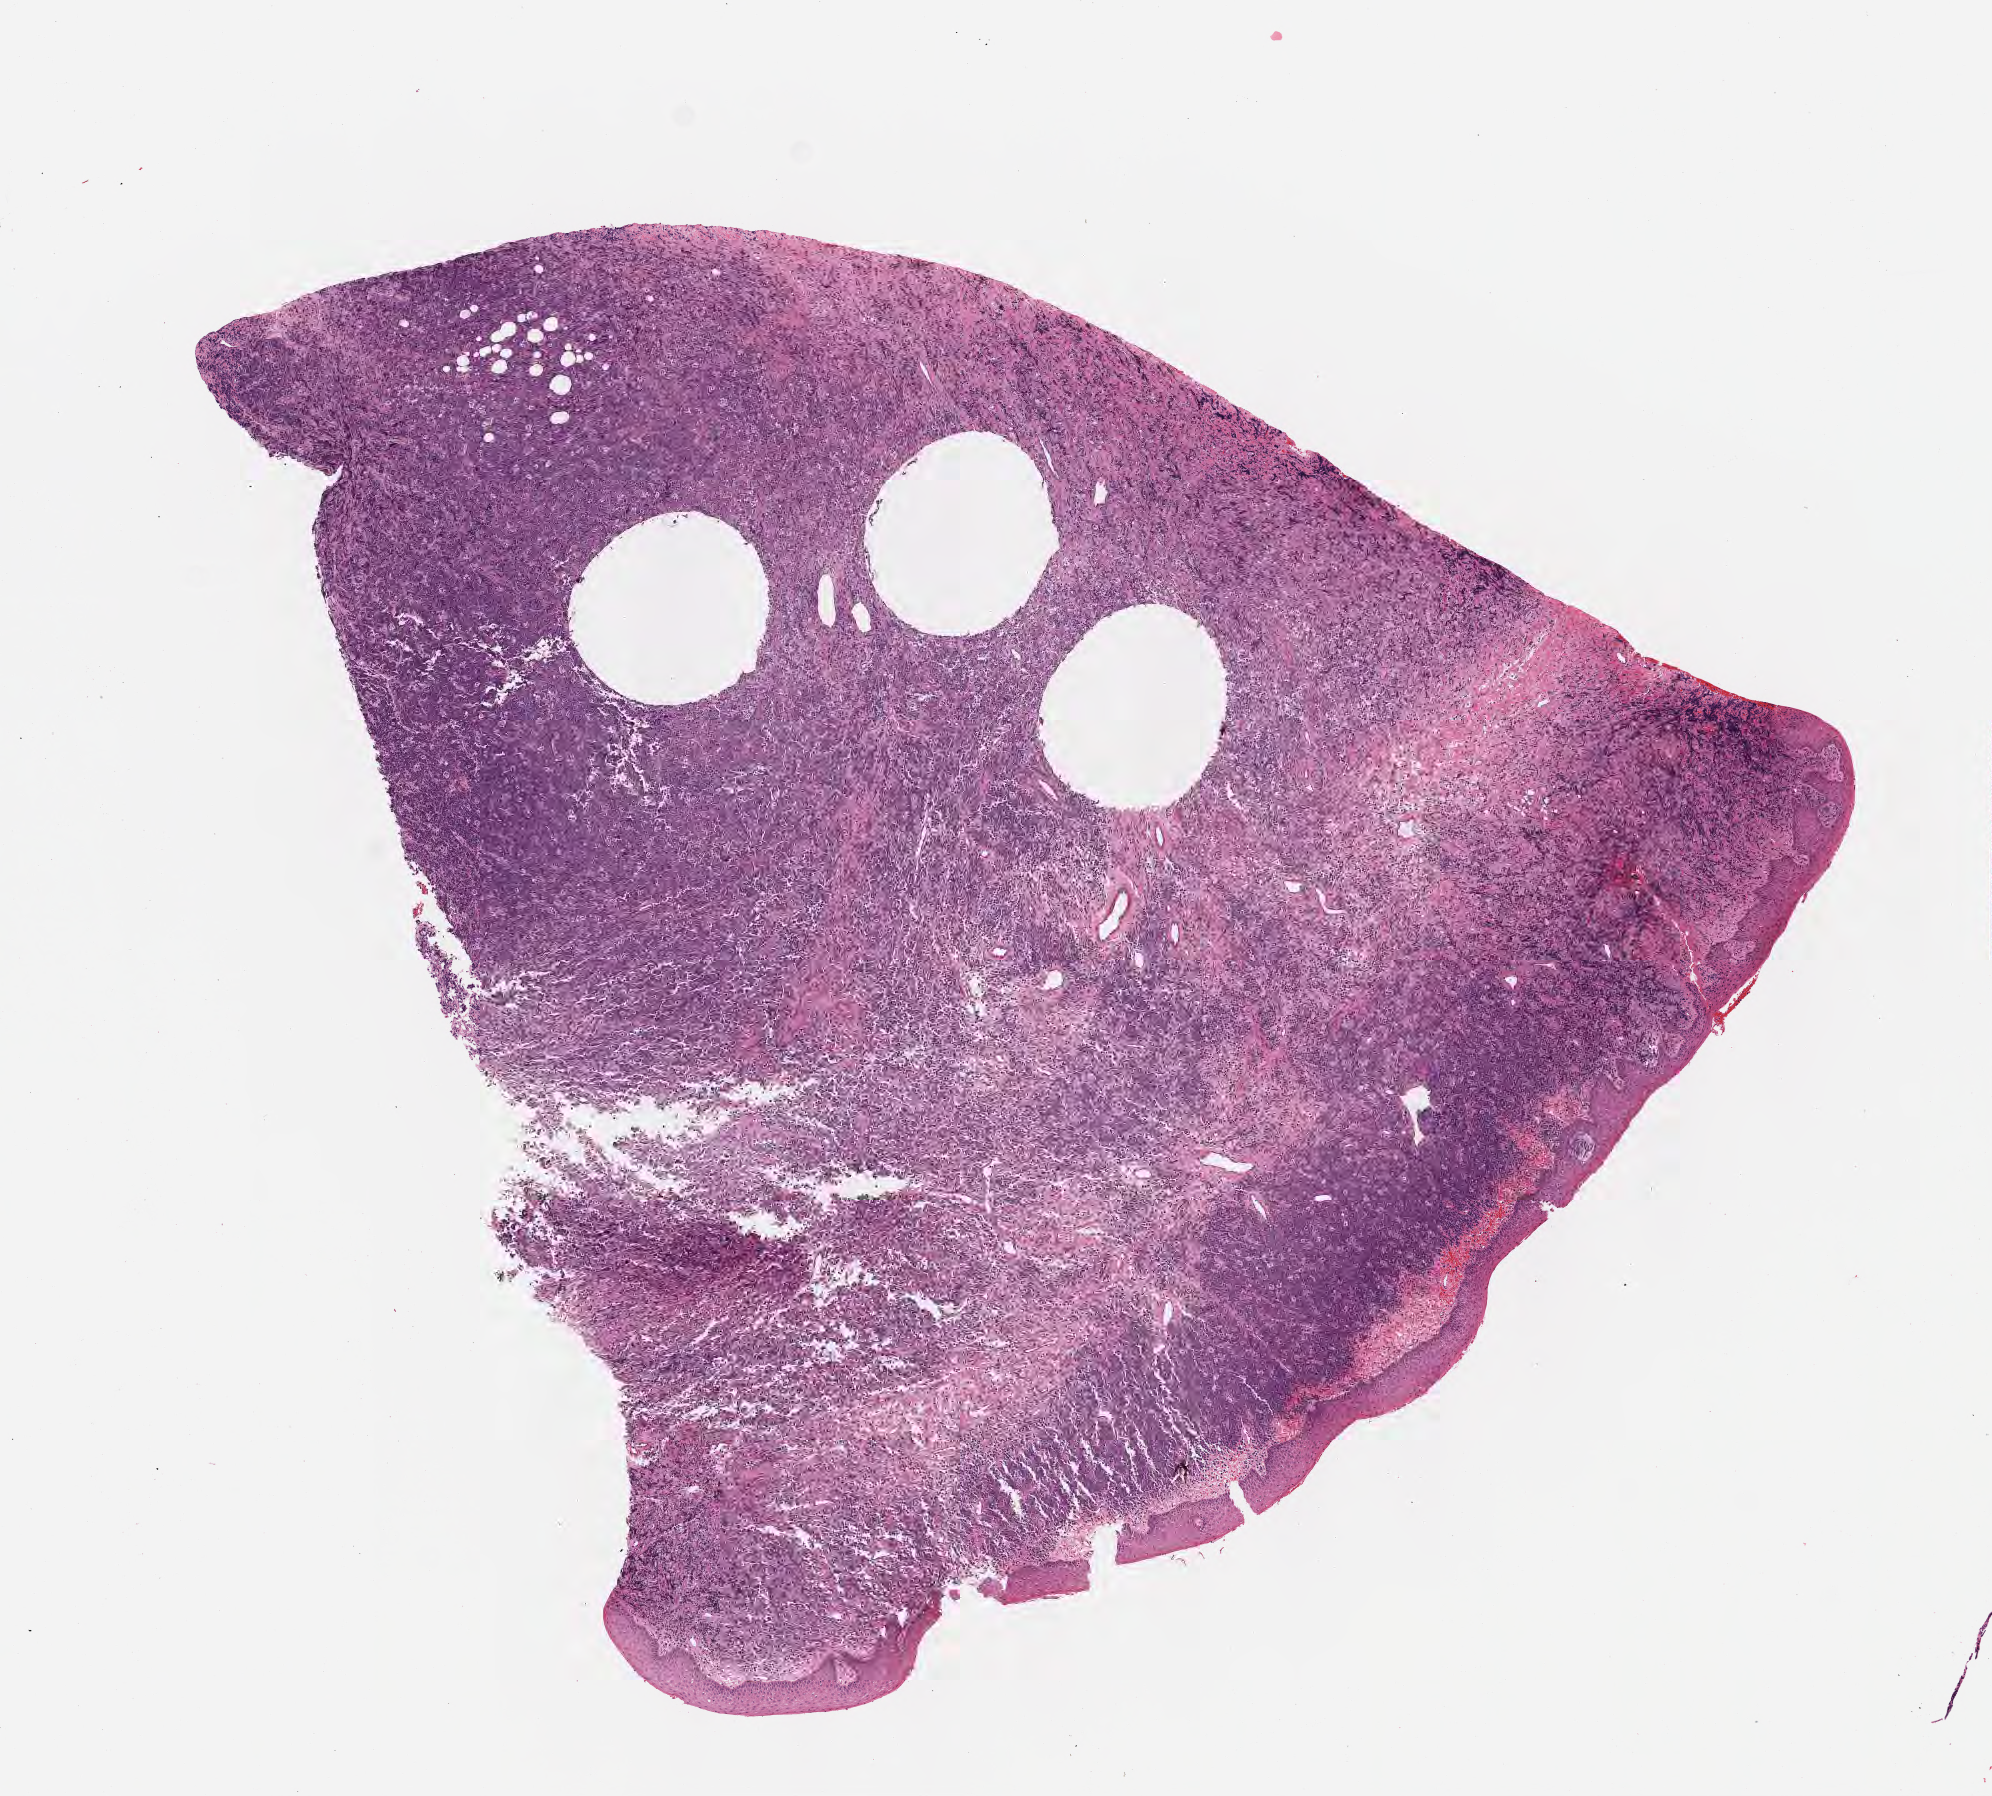
Digitized haematoxylin and eosin-stained section — low-resolution overview of the scanned area, about 8.0 x 7.3 mm, FFPE section, specimen: primary tumor, site: cranium. Patient: male, age at initial diagnosis 5 years. Slide review estimates, as recorded: tumor cells 70%, tumor nuclei 90%, stromal cells 10%, necrosis 10%, normal cells 10%. Infiltration values recorded for this section: lymphocyte infiltration 50%, monocyte infiltration 20%, neutrophil infiltration 10%.
* Ann Arbor stage (patient): Stage IV
* histologic diagnosis: Diffuse large B-cell lymphoma, NOS
* section: top of the tissue portion